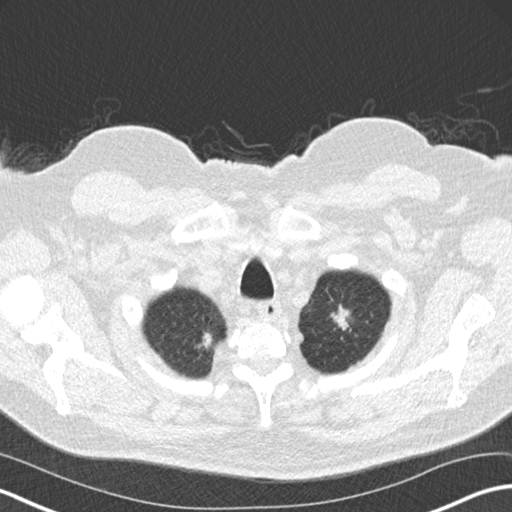
Low-dose screening chest CT, one axial slice; slice 153 of 175 in the series (ordered by position); reconstruction kernel B30f; lung window (W 1500 / L -600 HU); 512 × 512 image matrix.
Outlined on this slice (outlined manually by an expert reader):
- lesion 1 (tumor, upper lobe of left lung): bounding box <331,304,349,330> (left, top, right, bottom; pixels)